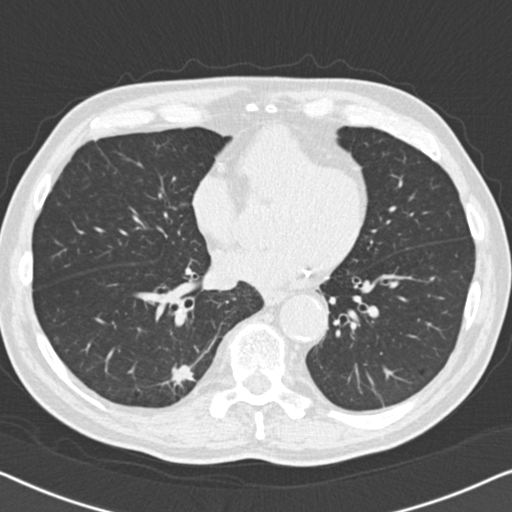
Chest CT (low-dose screening protocol), one axial image; second annual screen; lung window (W 1500 / L -600 HU); 2 mm slice thickness; standard (soft-tissue) reconstruction kernel (B30f); 120 kVp; 512 × 512 image matrix, field of view 330 × 330 mm. Male participant, aged 74 years at enrolment. Current smoker at enrolment.
• Lesion marked by an expert reader, box from (x=147, y=341) to (x=217, y=409) px.
• The screening reader recorded 5 non-calcified nodules or masses ≥4 mm on this exam (right lower lobe, right lower lobe, right lower lobe, left lower lobe, left lower lobe); which of them this box marks is not recorded.
• Participant outcome: lung cancer diagnosed 55 days after this screen — bronchiolo-alveolar adenocarcinoma, NOS, right lower lobe, moderately differentiated (G2), stage IA (AJCC 6th edition), 16 mm at pathology.